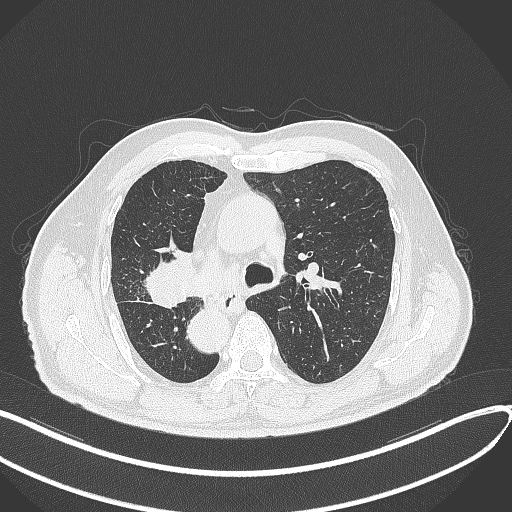
Chest CT, one axial slice. Position 204 of 300 along the scan axis. Reconstruction kernel B70f. Lung window (W 1500 / L -600 HU). 512 × 512 image matrix, field of view 400 × 400 mm. Male patient, age 67 years. From the clinical record (not read from this slice): clinical TNM (as recorded): T2a N0 M0.
Annotated regions visible in this slice (rectangle marked by the reading radiologist):
- lung tumour (recorded histology: squamous cell carcinoma): bounding box (x1, y1, x2, y2) in pixels: (138, 243, 196, 313)